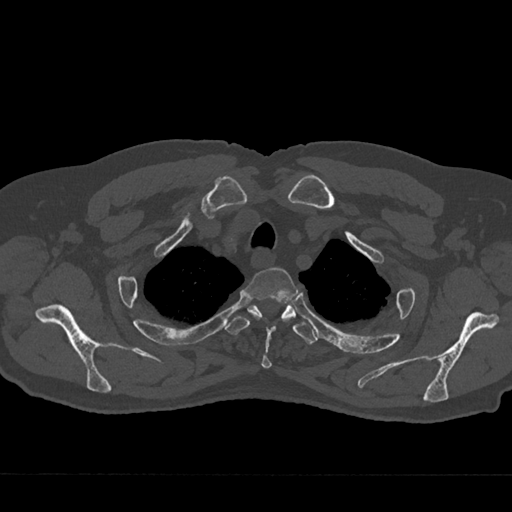
CT including the spine, one axial slice; slice 590 of 797 in the series (ordered by position); bone window (W 1800 / L 400 HU); 0.5 mm slice thickness; 512 × 512 image matrix, field of view 377 × 377 mm. Patient: male, 75 years. Case-level facts recorded for this patient, not image findings: primary cancer: renal; vertebrae with lytic lesions (as recorded): T4.
Annotated regions visible in this slice (semi-automatically segmented with operator editing):
- T2 vertebra: bounding box [x1, y1, x2, y2] px = [243, 267, 298, 369]
- T3 vertebra: [226, 304, 318, 345]